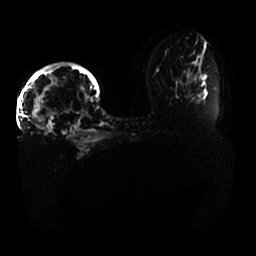
Breast MRI, one axial slice; slice 19 of 33 in the series (ordered by position); diffusion-weighted series; image 2 of 4 stored at this slice position (different b-values; order by instance number); 1.5 T; 4 mm slice thickness; 256 × 256 image matrix, field of view 400 × 400 mm. Female patient.
Annotated regions visible in this slice (expert manual segmentation):
- tumour on diffusion-weighted imaging: bounding box <29,94,46,128> (left, top, right, bottom; pixels)